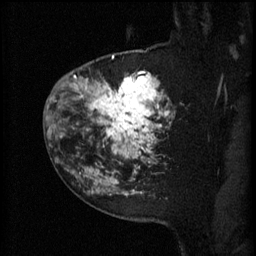
Breast MRI (dynamic contrast-enhanced), one sagittal slice. 3 images stored at this slice position (order not interpretable as contrast timing). 1.5 T. TE 4.2 ms, TR 11 ms. 2 mm slice thickness. 256 × 256 image matrix. Female patient, age 52 years.
Annotated regions visible in this slice (semi-automatically segmented with operator editing):
- analysis volume of interest (the breast-tissue region the enhancement analysis was run in; not a lesion): bounding box <81,52,174,157> (left, top, right, bottom; pixels)
- tumour enhancement mask (voxels above the 70 % enhancement threshold inside the analysis volume of interest): <81,56,171,157>